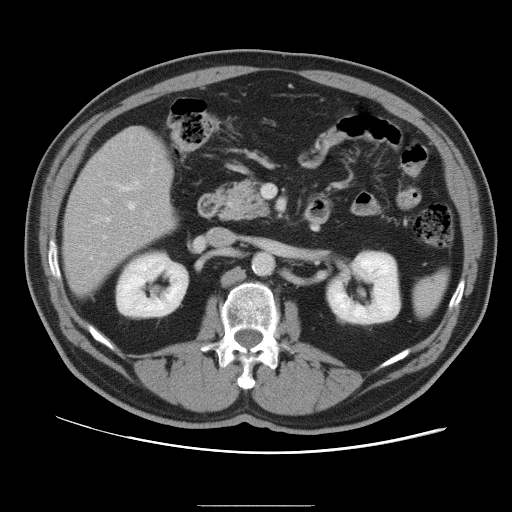
Contrast-enhanced abdominal CT, one axial slice; position 45 of 105 along the scan axis; 120 kVp; intravenous contrast given; soft-tissue window (W 400 / L 40 HU); 512 × 512 image matrix. Male patient, age 64 years. From the clinical record (not read from this slice): diagnosis: colorectal cancer liver metastases, imaged before liver resection; multiple liver metastases: yes; largest metastasis: 3 cm; chemotherapy before resection: yes.
Outlined on this slice (manually delineated by an expert):
- hepatic veins: bounding box (x1, y1, x2, y2) in pixels: (90, 202, 135, 259)
- liver: (64, 128, 176, 295)
- planned liver remnant (the part of the liver to remain after resection): (66, 128, 177, 296)
- portal vein (with intrahepatic branches): (103, 180, 140, 254)